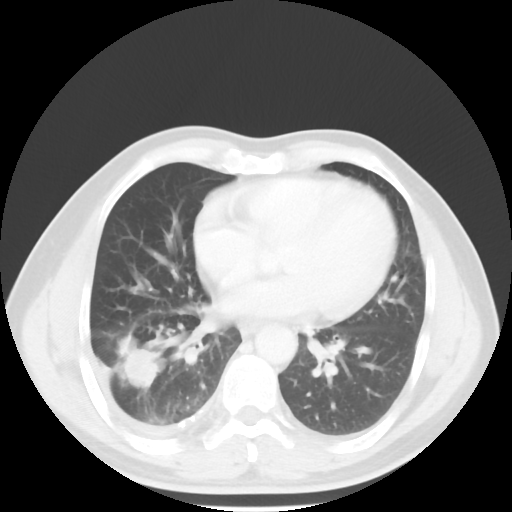
Chest CT, one axial slice. Position 23 of 56 along the scan axis. Lung window (W 1500 / L -600 HU). 5 mm slice thickness. 512 × 512 image matrix, field of view 344 × 344 mm. Patient: male, 56 years. Case-level facts recorded for this patient, not image findings: clinical TNM (as recorded): T2 N3 M1.
Annotated regions visible in this slice (rectangle marked by the reading radiologist):
- lung tumour (recorded histology: adenocarcinoma): bounding box (x1, y1, x2, y2) in pixels: (115, 340, 159, 392)